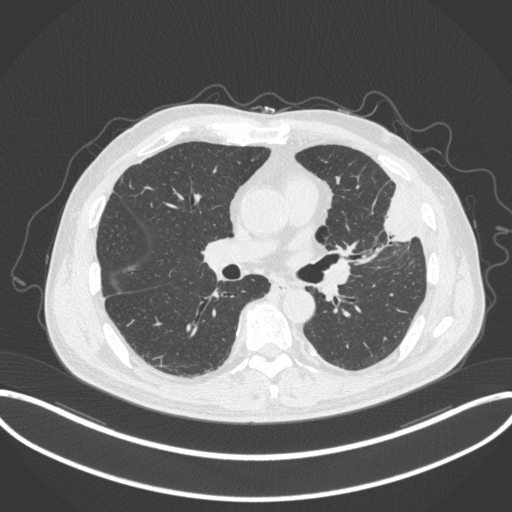
Chest CT, one axial slice. Slice 180 of 382 in the series (ordered by position). Reconstruction kernel B31f. Lung window (W 1500 / L -600 HU). 1 mm slice thickness. 512 × 512 image matrix, field of view 415 × 415 mm. Male patient, age 64 years. From the clinical record (not read from this slice): clinical TNM (as recorded): T4 N1 M0.
Outlined on this slice (rectangle marked by the reading radiologist):
- lung tumour (recorded histology: adenocarcinoma): bounding box (x1, y1, x2, y2) in pixels: (381, 182, 419, 244)